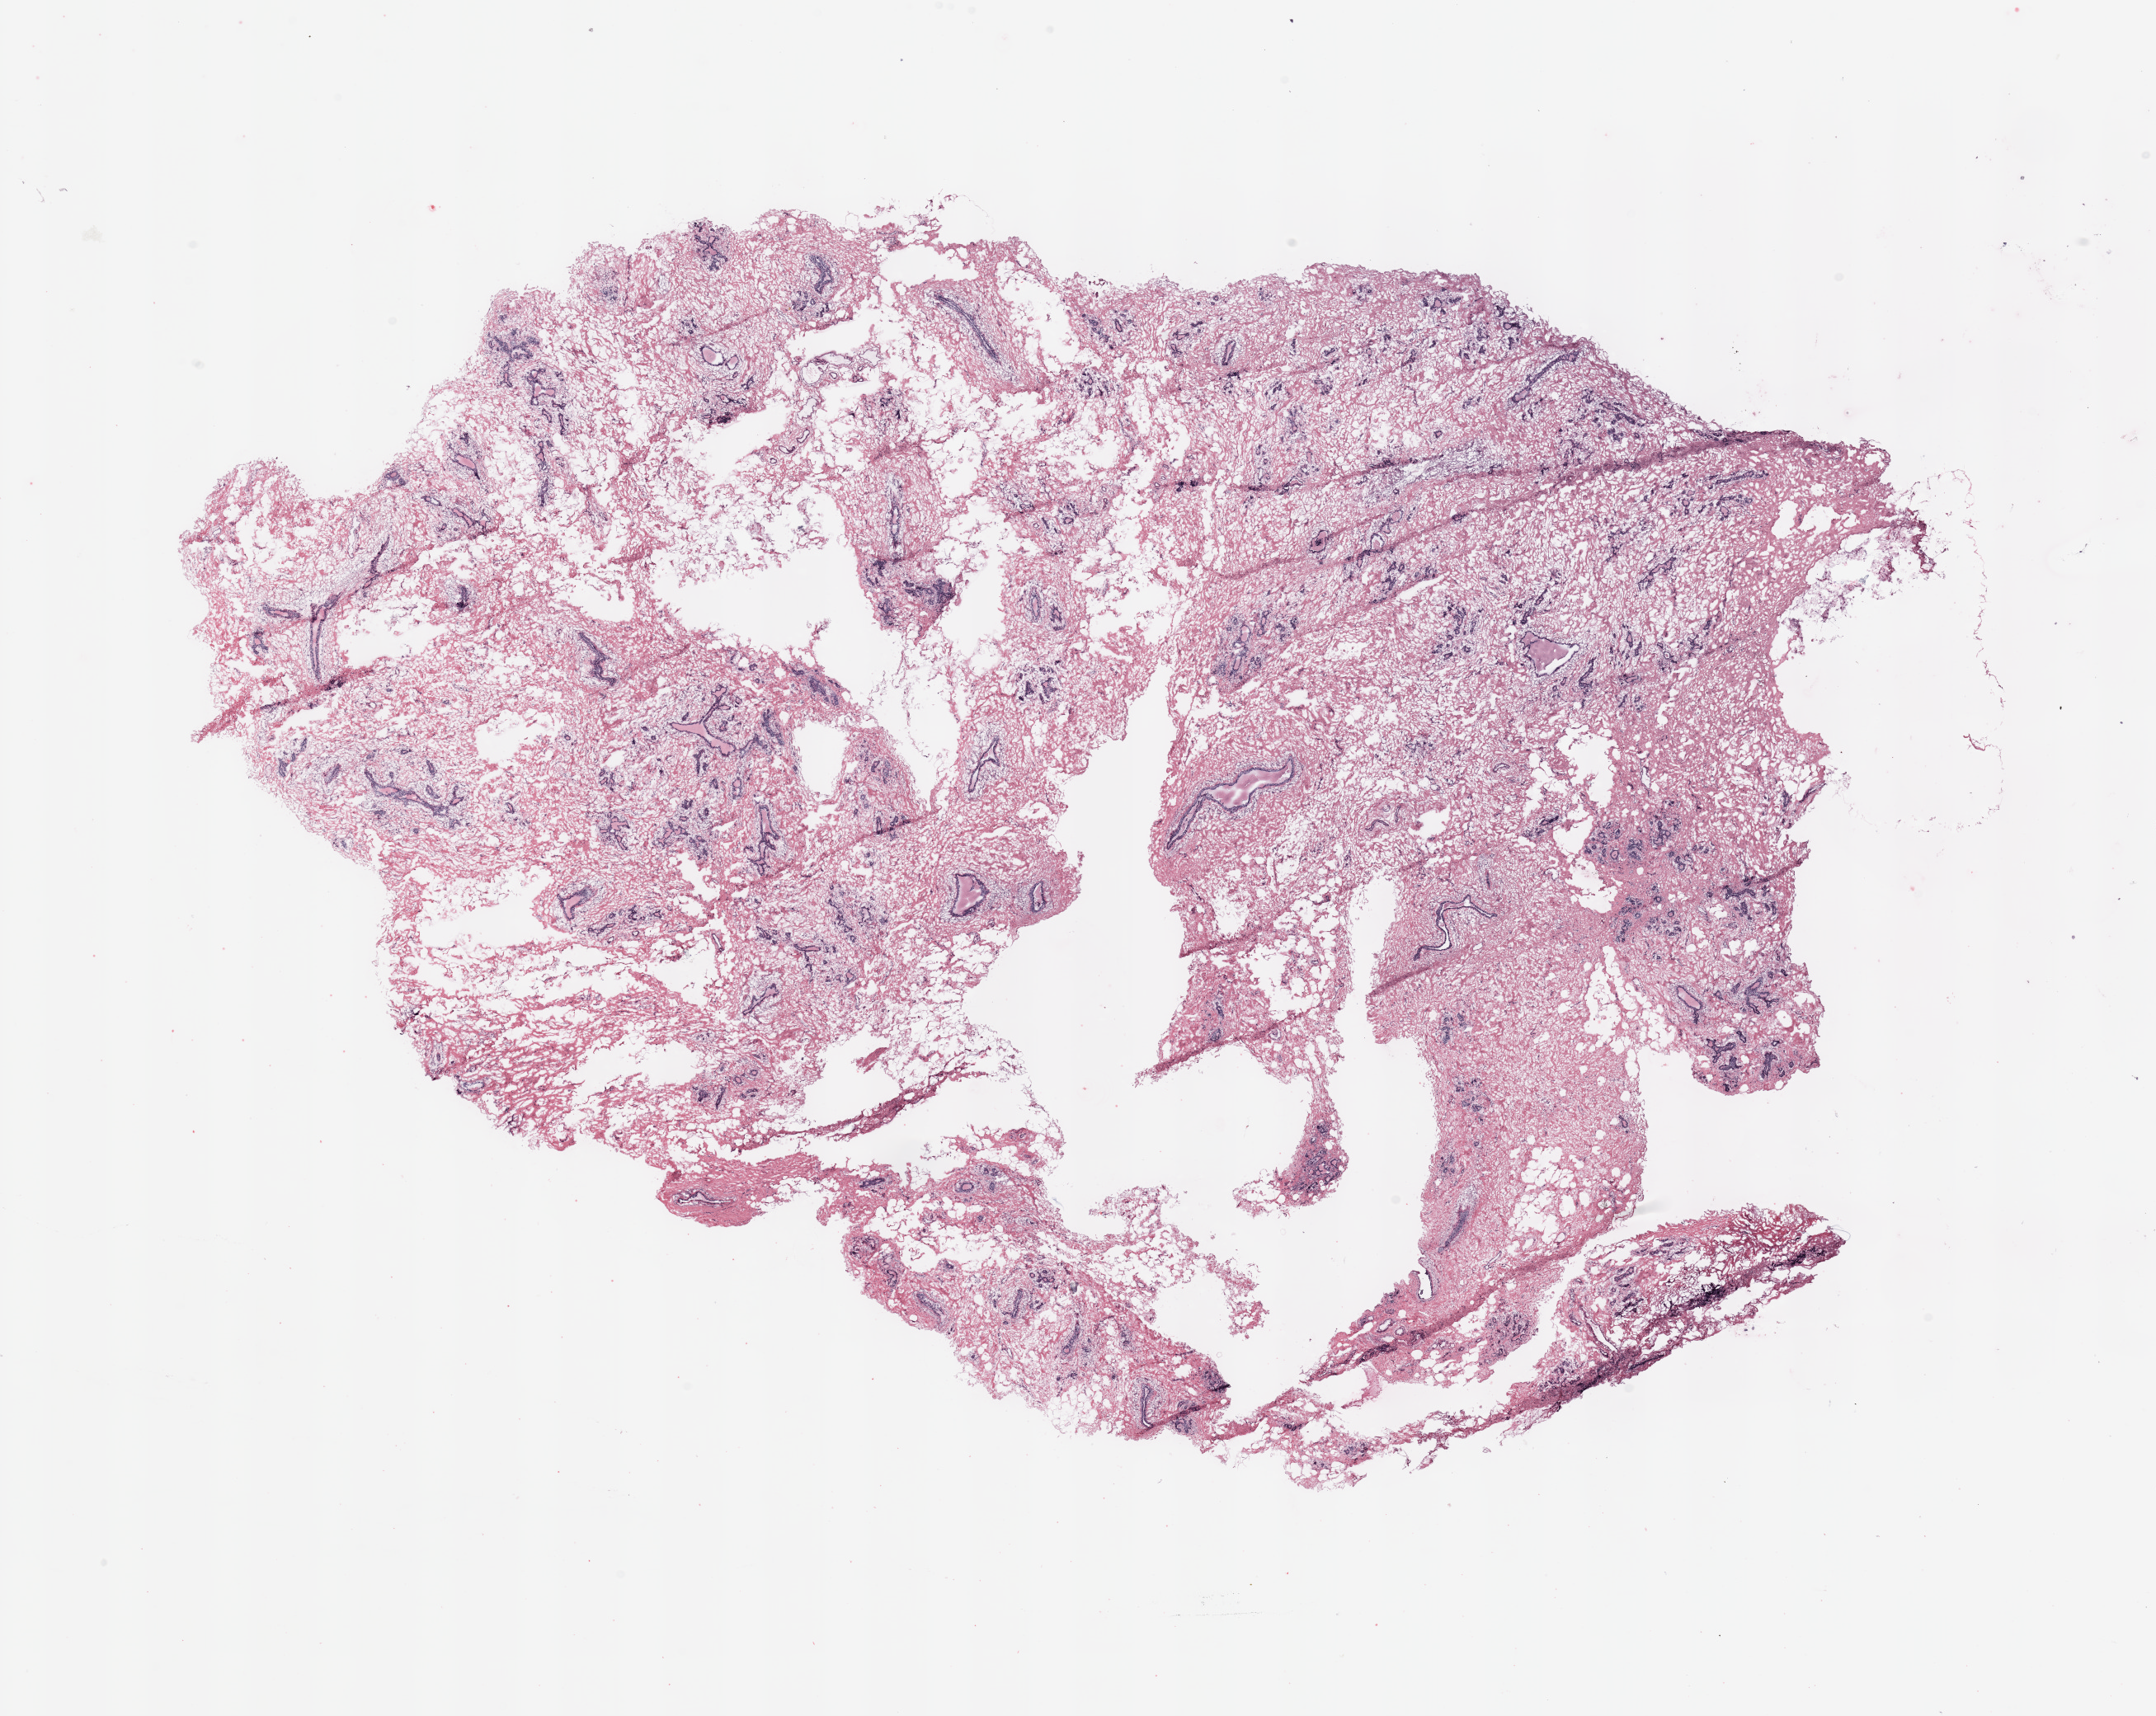
Whole-slide histology image, H&E-stained, a low-resolution overview of the entire scanned area, about 20.7 x 16.5 mm. Breast, tissue type not recorded.
- patient diagnosis (cohort enrolment): breast cancer (breast)